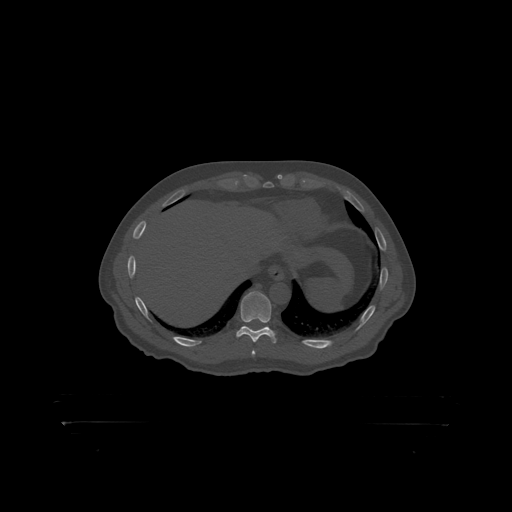
CT including the spine, one axial slice; reconstruction kernel STANDARD; bone window (W 1800 / L 400 HU); 512 × 512 image matrix, field of view 650 × 650 mm. Male patient, age 46 years. From the clinical record (not read from this slice): primary cancer: skin.
Annotated regions visible in this slice (semi-automatically segmented with operator editing):
- T10 vertebra: bounding box [x1, y1, x2, y2] px = [241, 292, 272, 319]